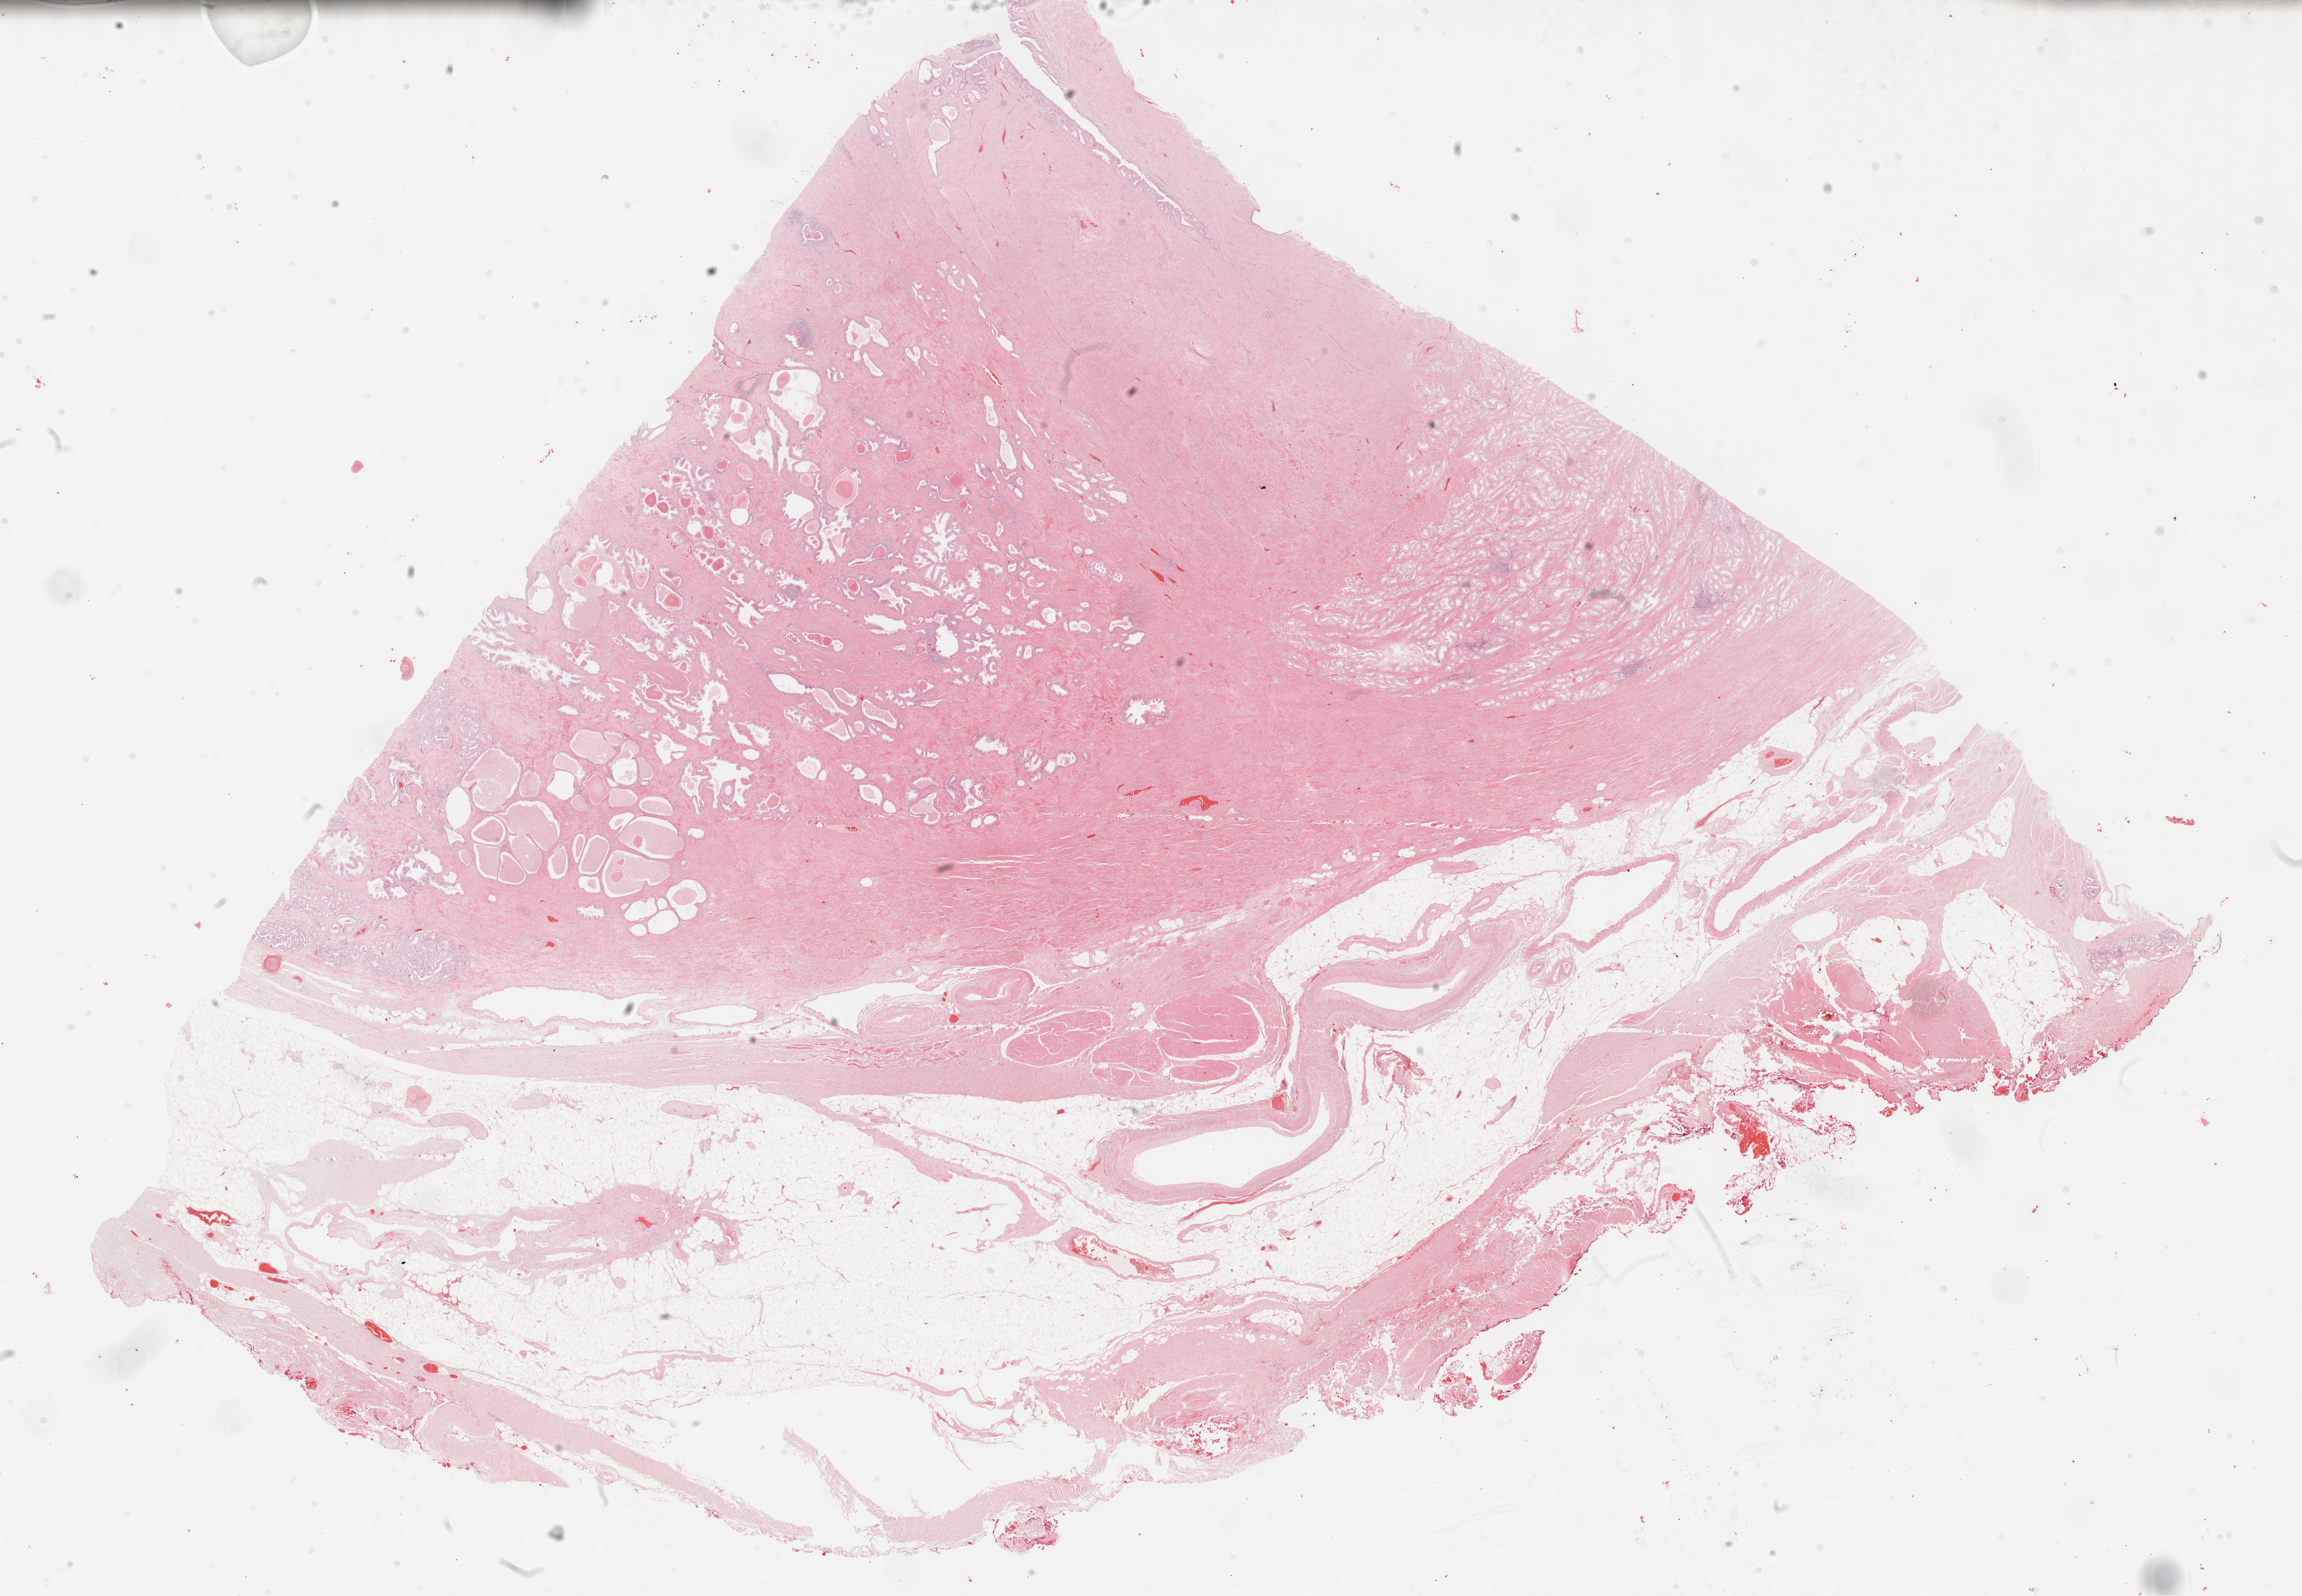
Whole-slide histology image, H&E-stained — low-resolution overview of the scanned area, about 30.7 x 21.3 mm (from a 40x scan); formalin-fixed paraffin-embedded (FFPE) diagnostic section; primary tumour sample from the prostate. Male patient; age at initial diagnosis 72 years. Gleason score: 8 (4+4).
- pathologic diagnosis: Adenocarcinoma, NOS (prostate gland)
- lymph nodes positive (case pathology): 0 of 4 examined